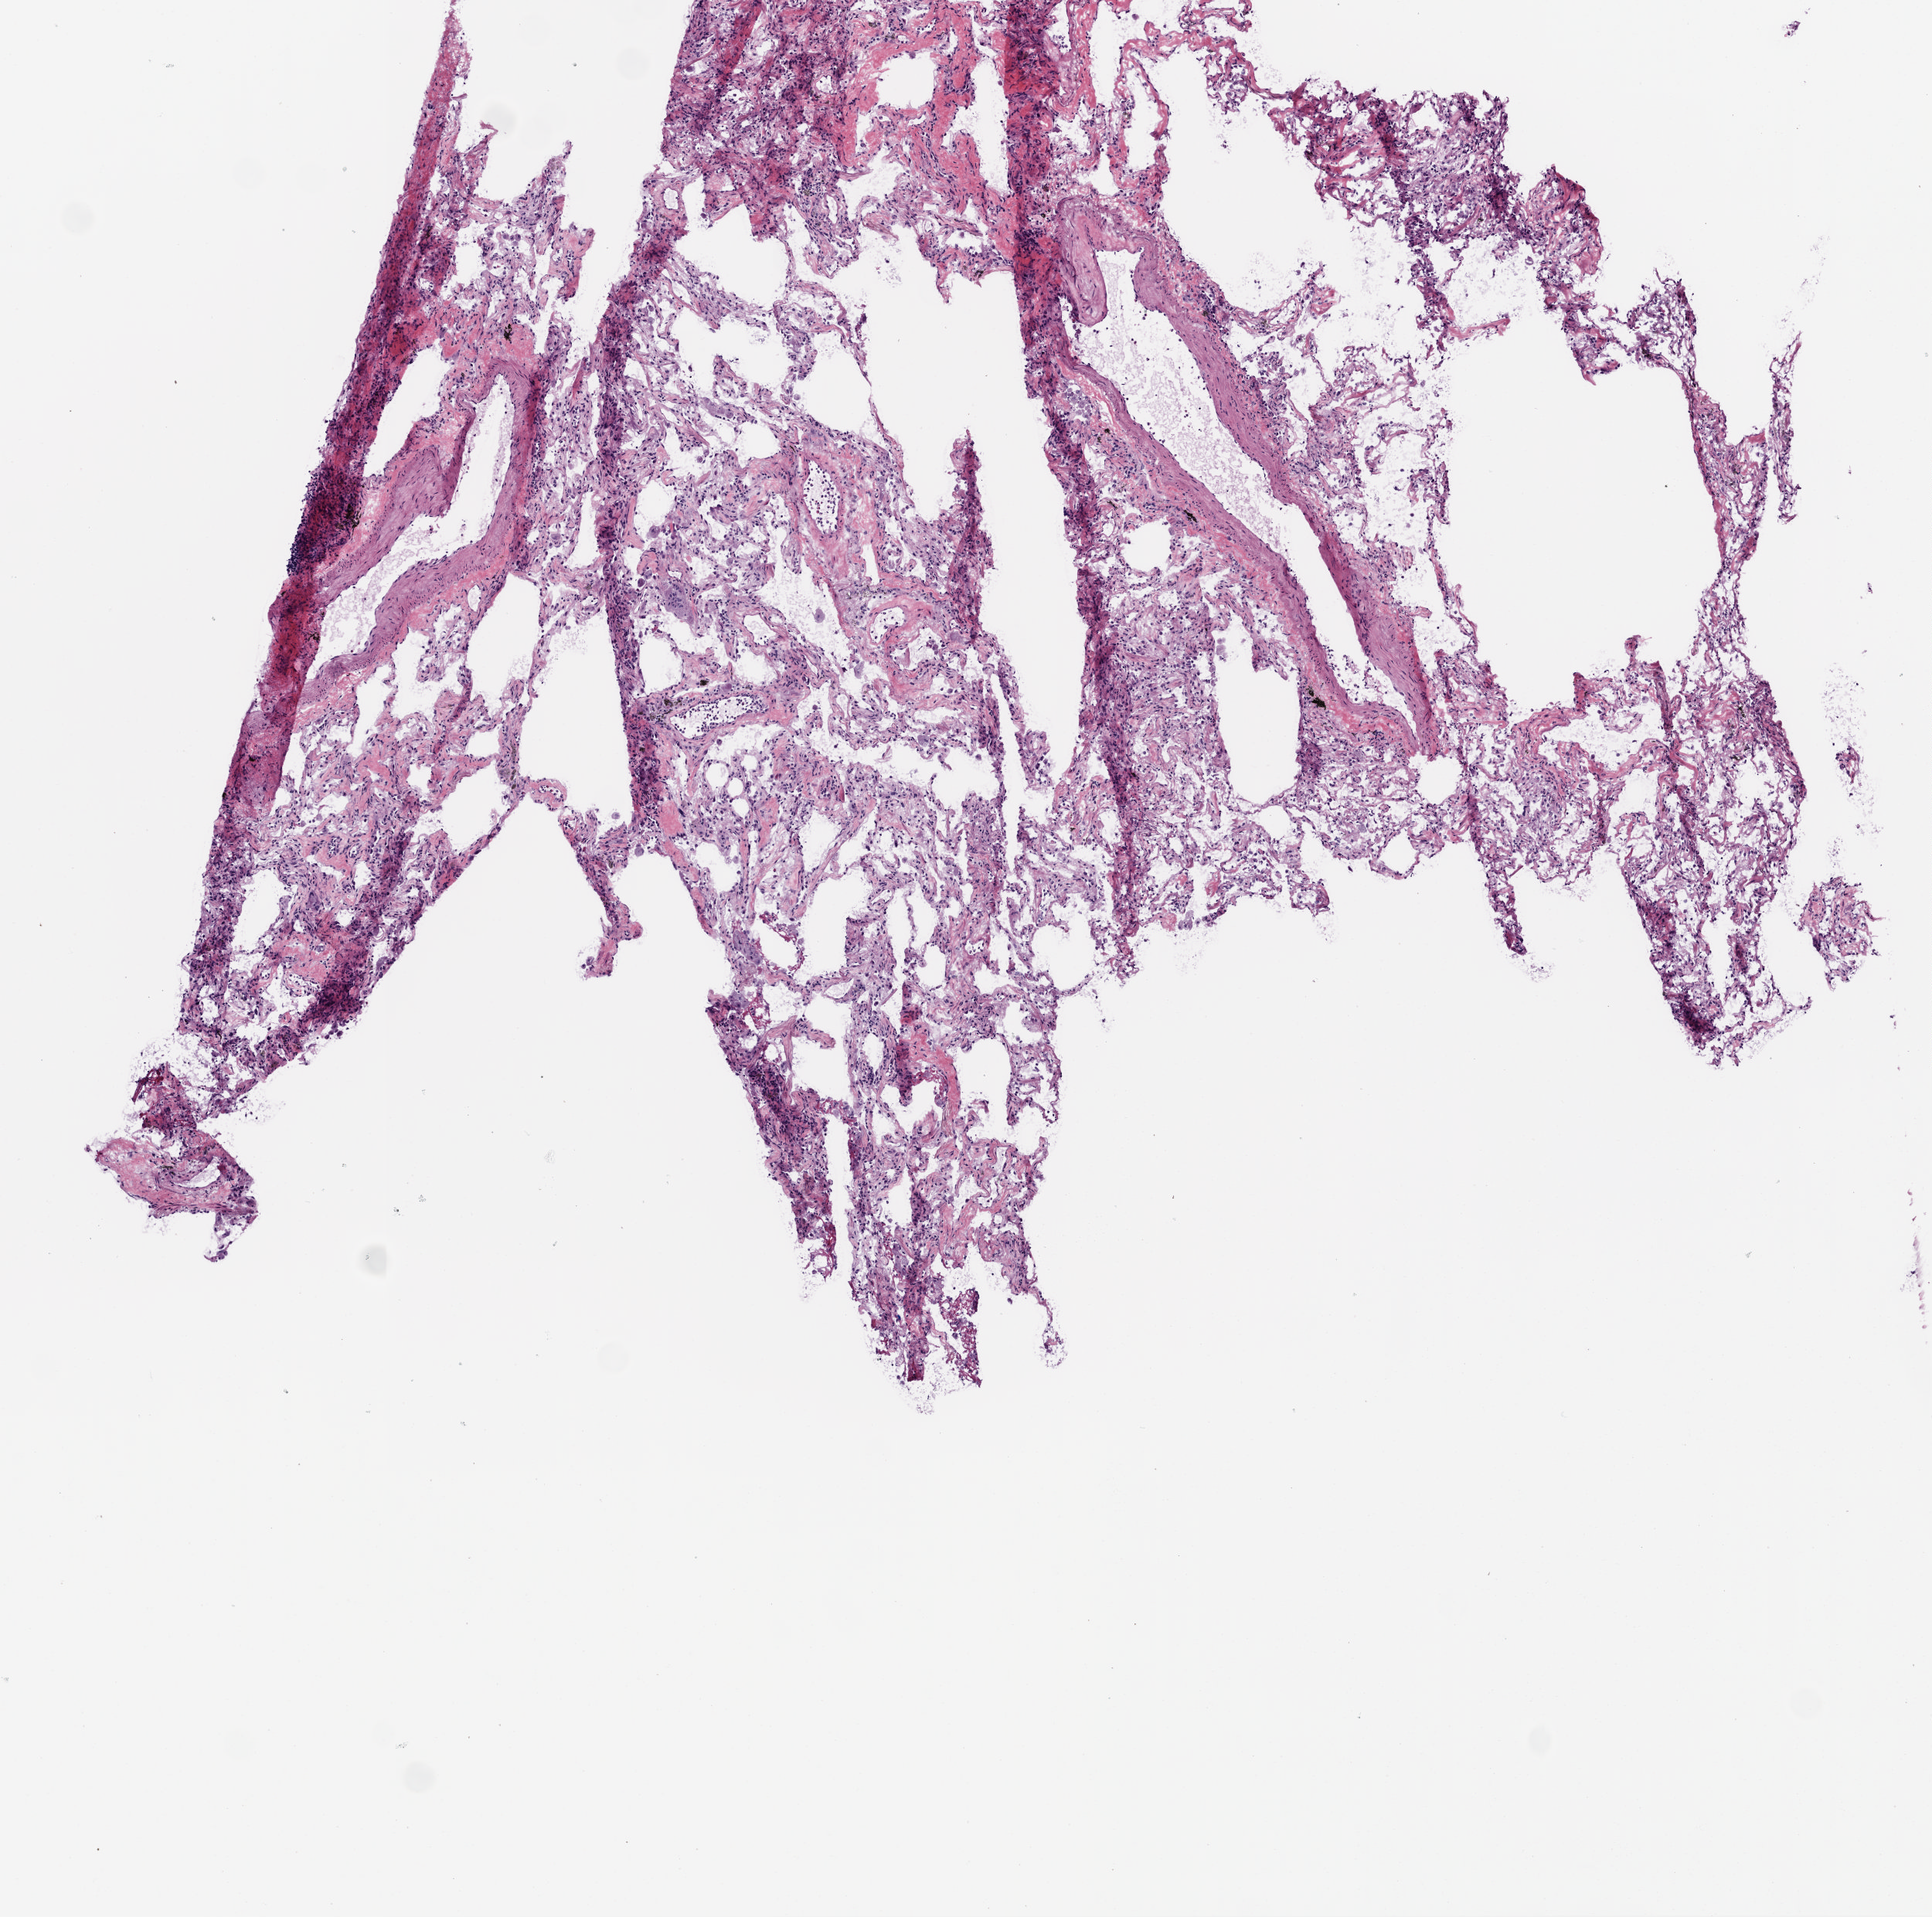
H&E whole-slide image, whole scanned area (about 5.0 x 5.0 mm) shown as a low-resolution overview; frozen section from the top of the tissue portion; sample: solid tissue normal (non-tumour tissue), lung. Patient: male, age at initial diagnosis 68 years.
This section: solid tissue normal (non-tumour) sample from the same patient. Patient diagnosis: Adenocarcinoma, NOS (upper lobe, lung).